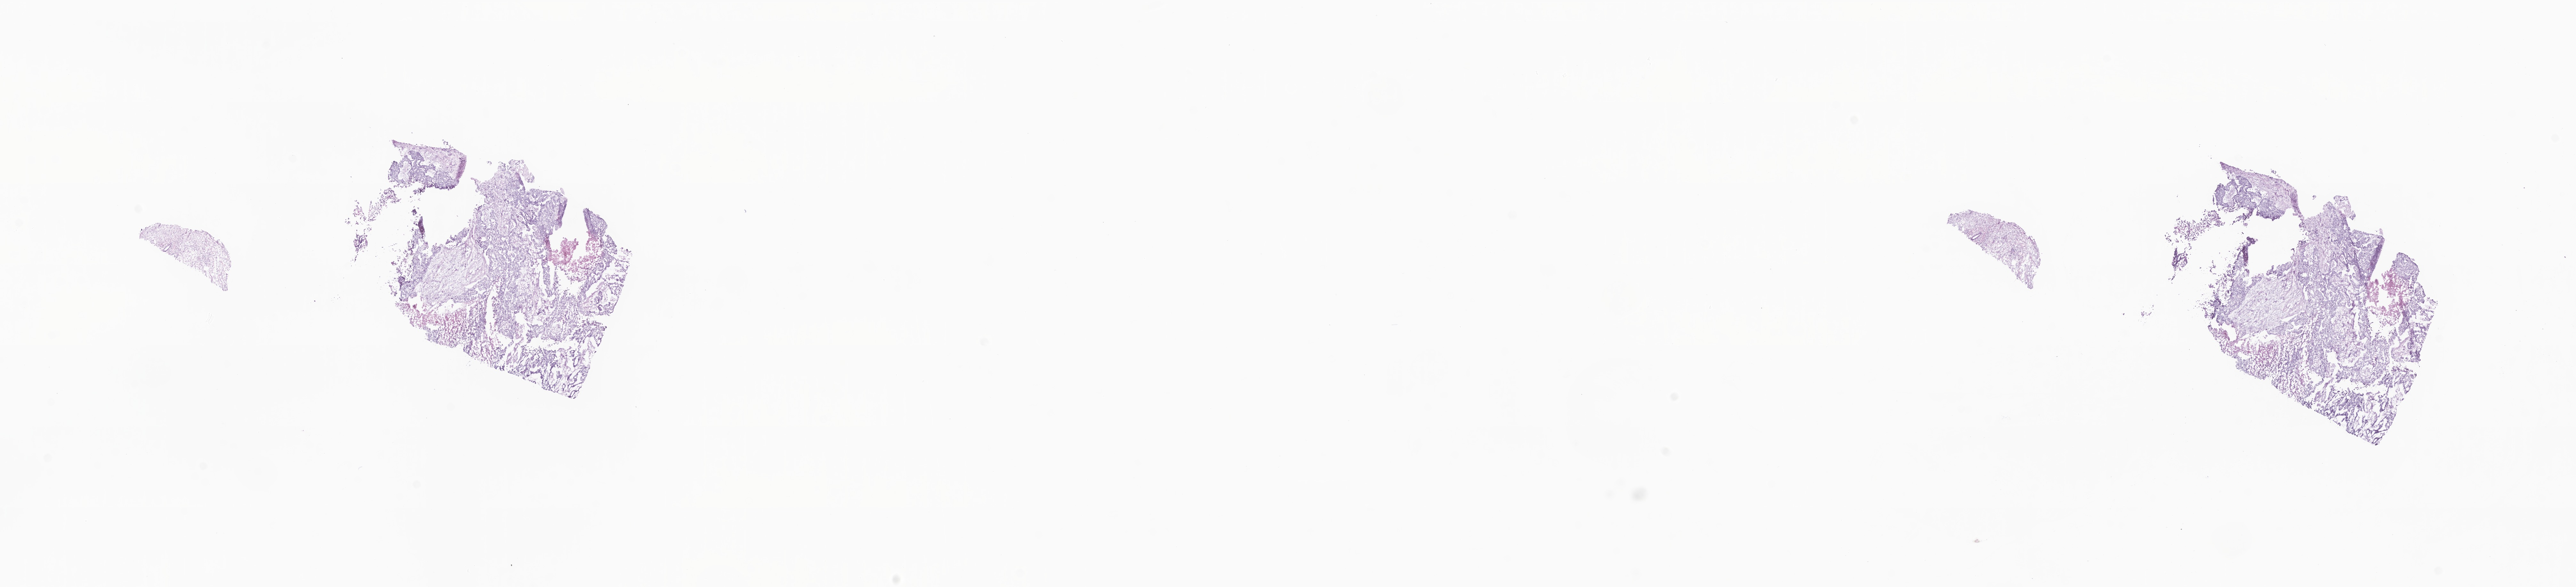
Whole-slide image, haematoxylin and eosin stain — low-resolution overview of the scanned area, about 33.9 x 7.7 mm, cryosection, metastatic tumor tissue. Male patient; age at initial diagnosis 34 years. Slide review estimates, as recorded: tumor cells 77%, tumor nuclei 89%, stromal cells 13%, necrosis 6%, normal cells 4%. Infiltration values recorded for this section: lymphocyte infiltration 0%, monocyte infiltration 0%, neutrophil infiltration 0%.
Section: bottom of the tissue portion. Patient diagnosis (primary): Adenocarcinoma, NOS.